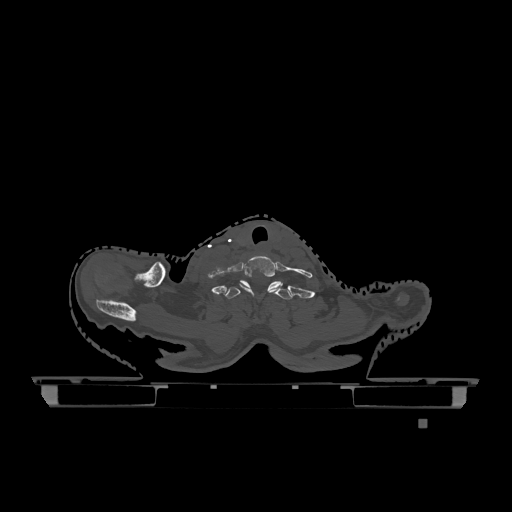
CT including the spine, one axial slice. Slice 1015 of 1317 in the series (ordered by position). Bone window (W 1800 / L 400 HU). 0.5 mm slice thickness. 512 × 512 image matrix. Female patient, age 74 years. From the clinical record (not read from this slice): primary cancer: lung.
Outlined on this slice (semi-automatic segmentation, software-assisted and operator-edited):
- T1 vertebra: bounding box [x1, y1, x2, y2] px = [223, 280, 292, 300]